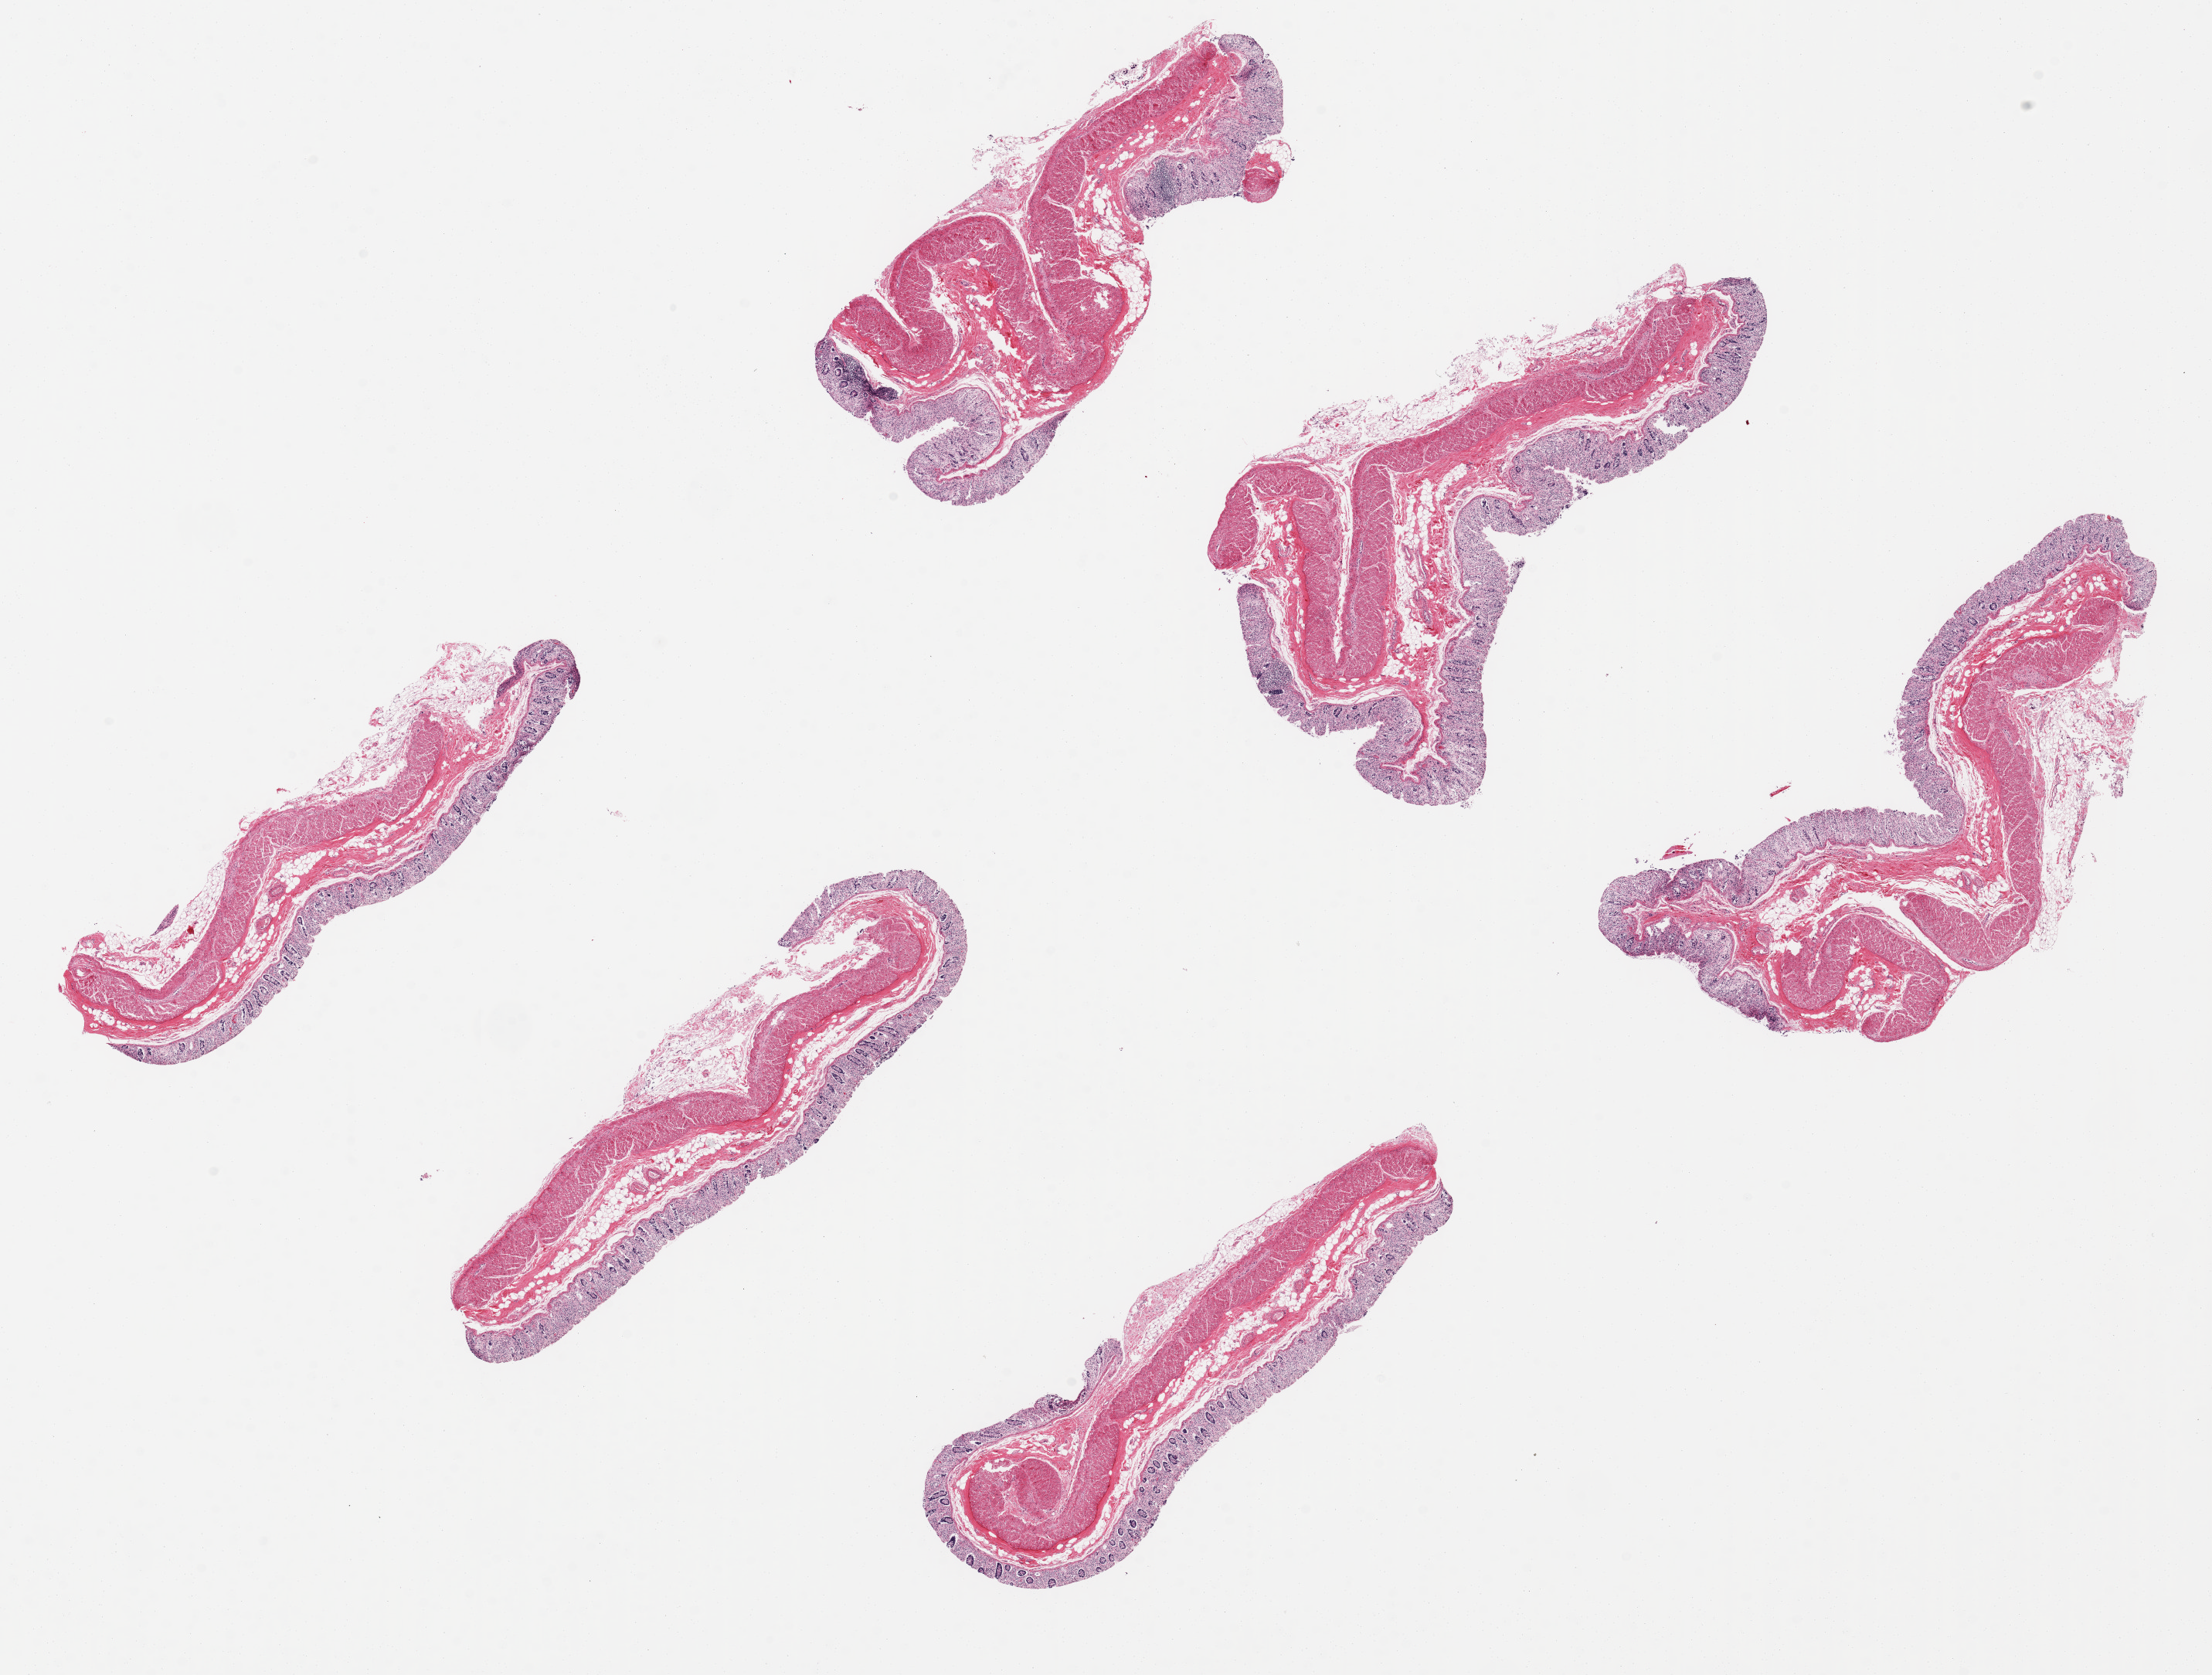
Digitized H&E-stained section, shown as a low-resolution overview of the whole scanned area (about 22.6 x 17.1 mm); PAXgene-fixed, paraffin-embedded tissue; section of transverse colon (target tissue); tissue donor sample.
• pathologist's review note for this sample: 6 pieces up to 6.7x2 mm; mucosa almost totally autolyzed; muscle slight to moderate fragmentation